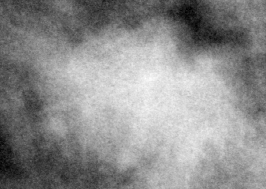
Cropped region of a digitized screen-film mammogram centred on a radiologist-marked abnormality, left breast, MLO view.
Marked abnormality: mass, shape lobulated, margins circumscribed; BI-RADS assessment category 4; subtlety rating 5 on a 1 (subtle) to 5 (obvious) scale; pathology (as recorded): benign.